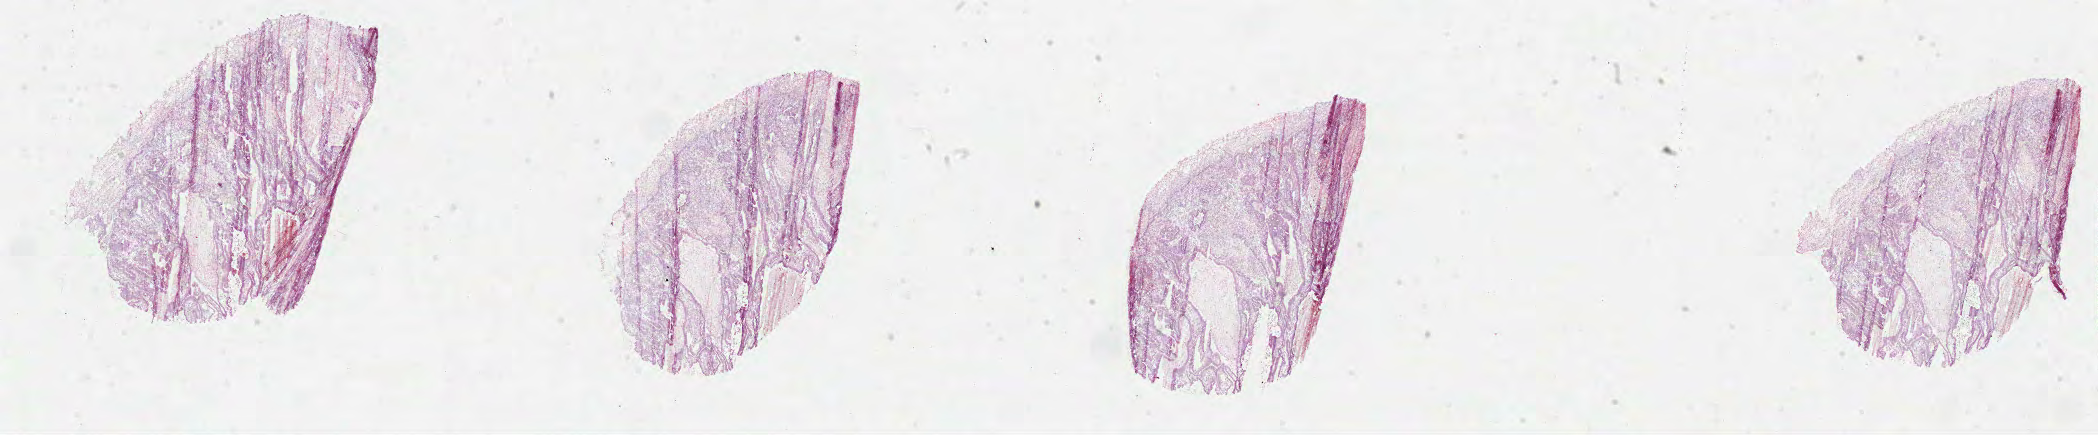
Whole-slide histology image, Hematoxylin and eosin (H&E) stained — shown as a low-resolution overview of the whole scanned area (about 33.8 x 7.0 mm), FFPE section, primary tumour sample from the stomach. Patient: male, age at initial diagnosis 64 years. Histologic grade: G2 (moderately differentiated).
• pathologic diagnosis: Tubular adenocarcinoma (body of stomach)
• AJCC pathologic stage: IIB